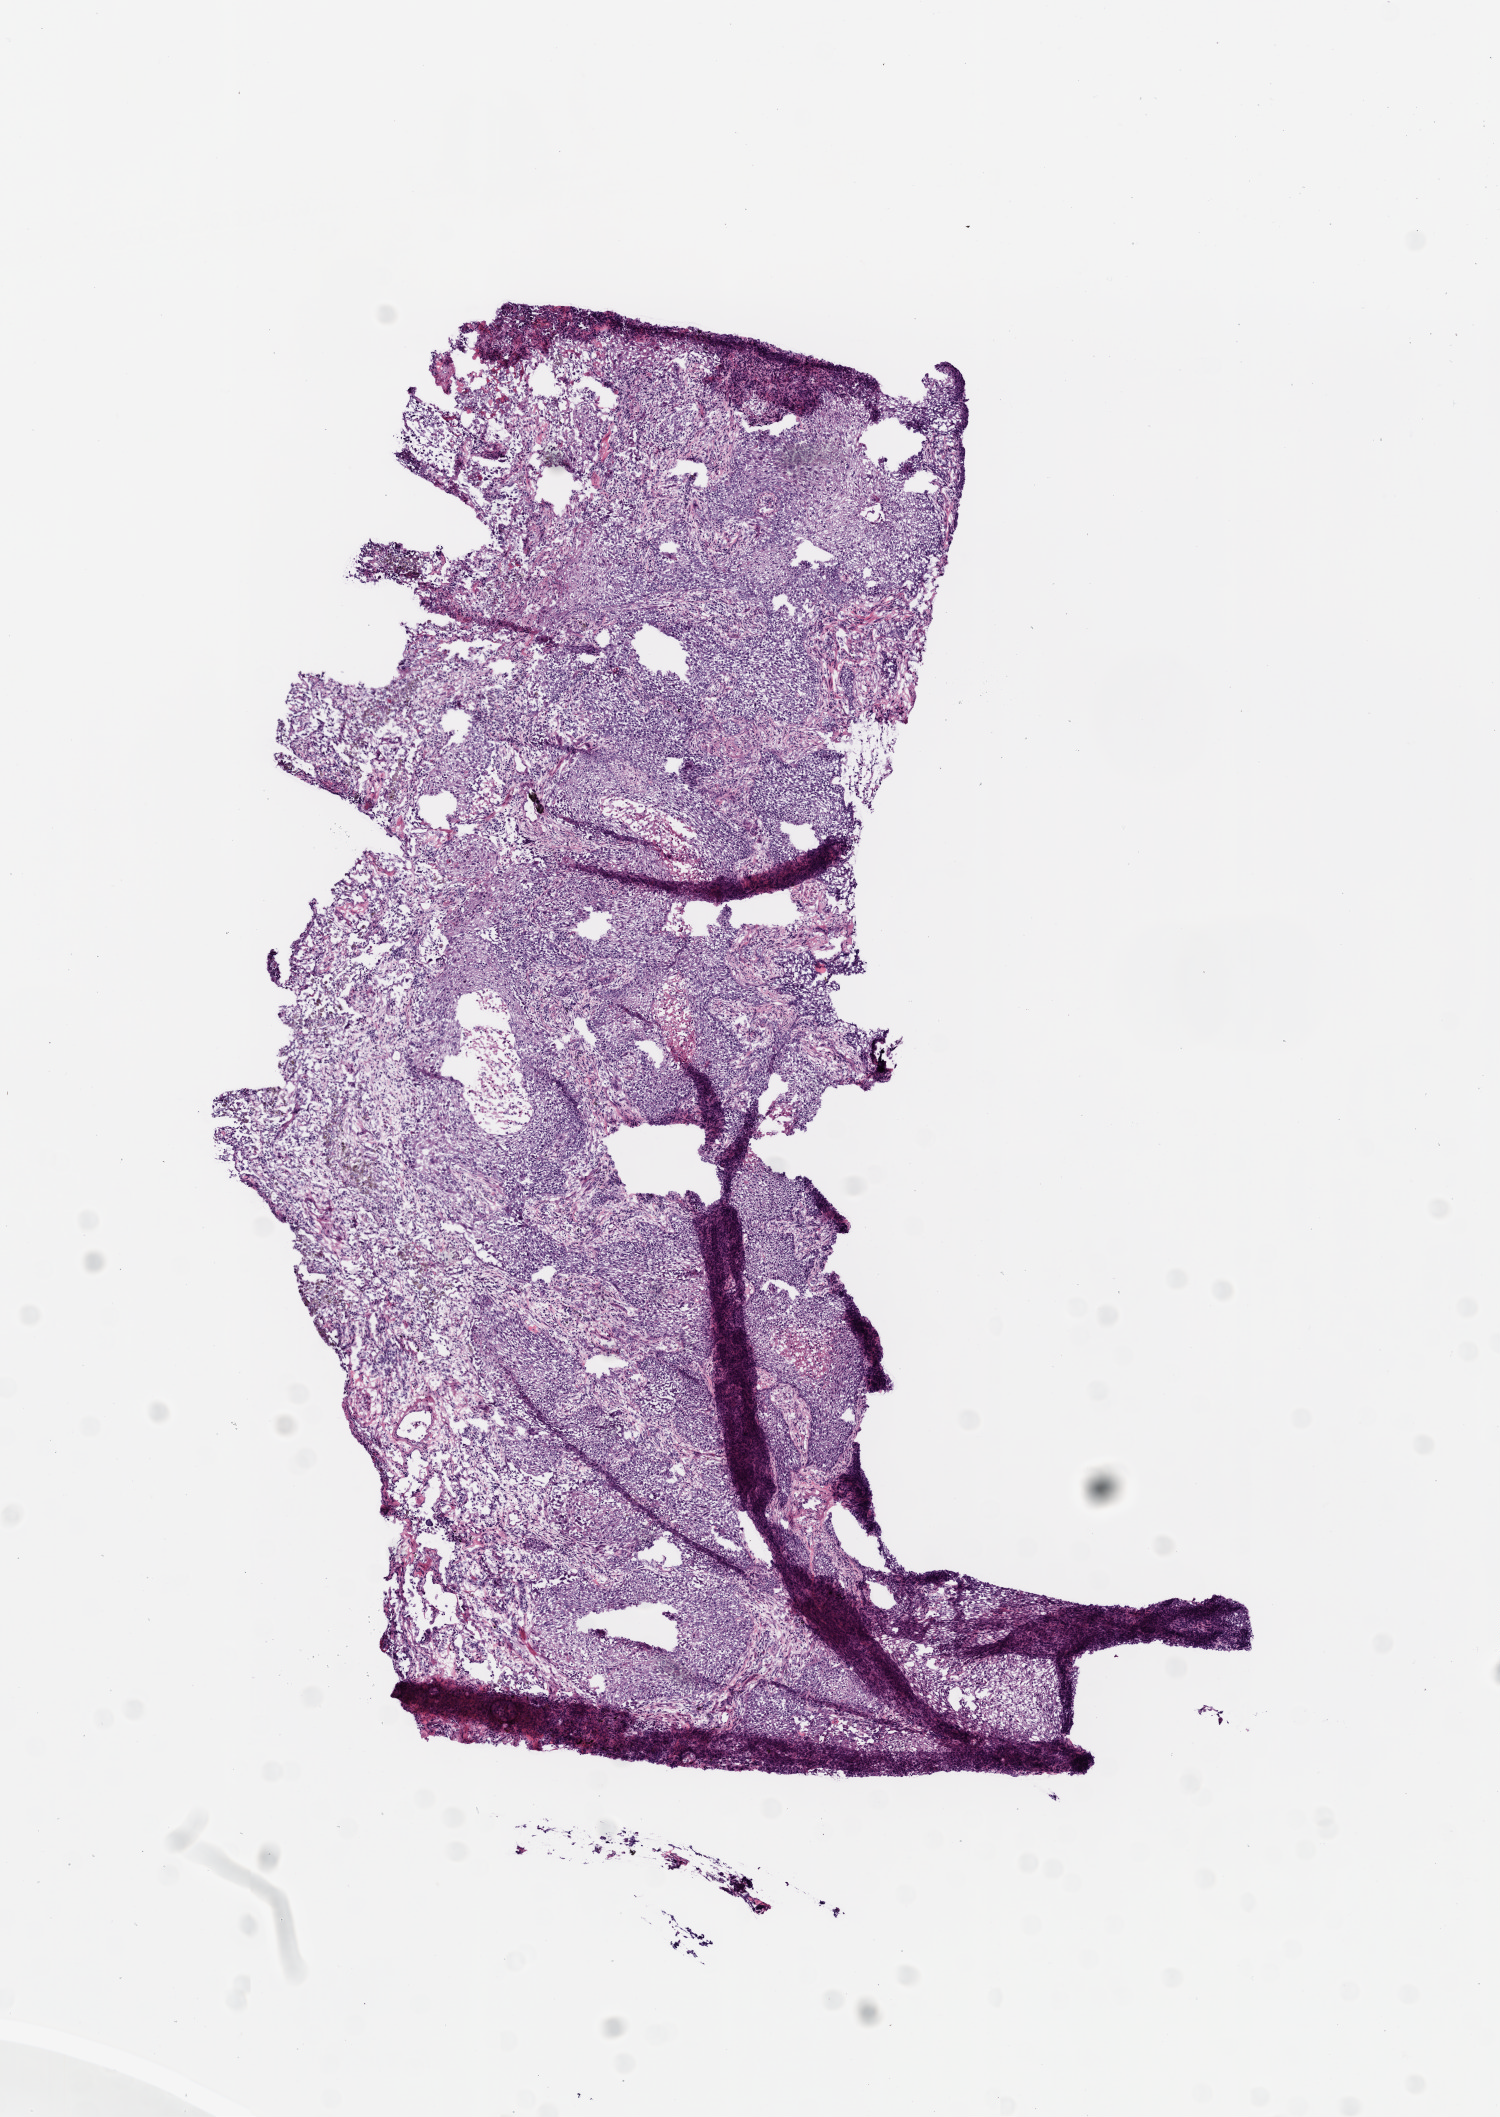
Digitized H&E-stained tissue section (whole slide), whole scanned area (about 6.0 x 8.5 mm) shown as a low-resolution overview. Frozen section. Lung, primary tumour sample. Patient: male, age at initial diagnosis 64 years. Slide review estimates, as recorded: tumour cells 70%, tumour nuclei 80%, normal cells 15%, stromal cells 5%, necrosis 10%.
Laterality: left. Pathologic diagnosis: Squamous cell carcinoma, NOS (lower lobe, lung). AJCC pathologic stage: IB.